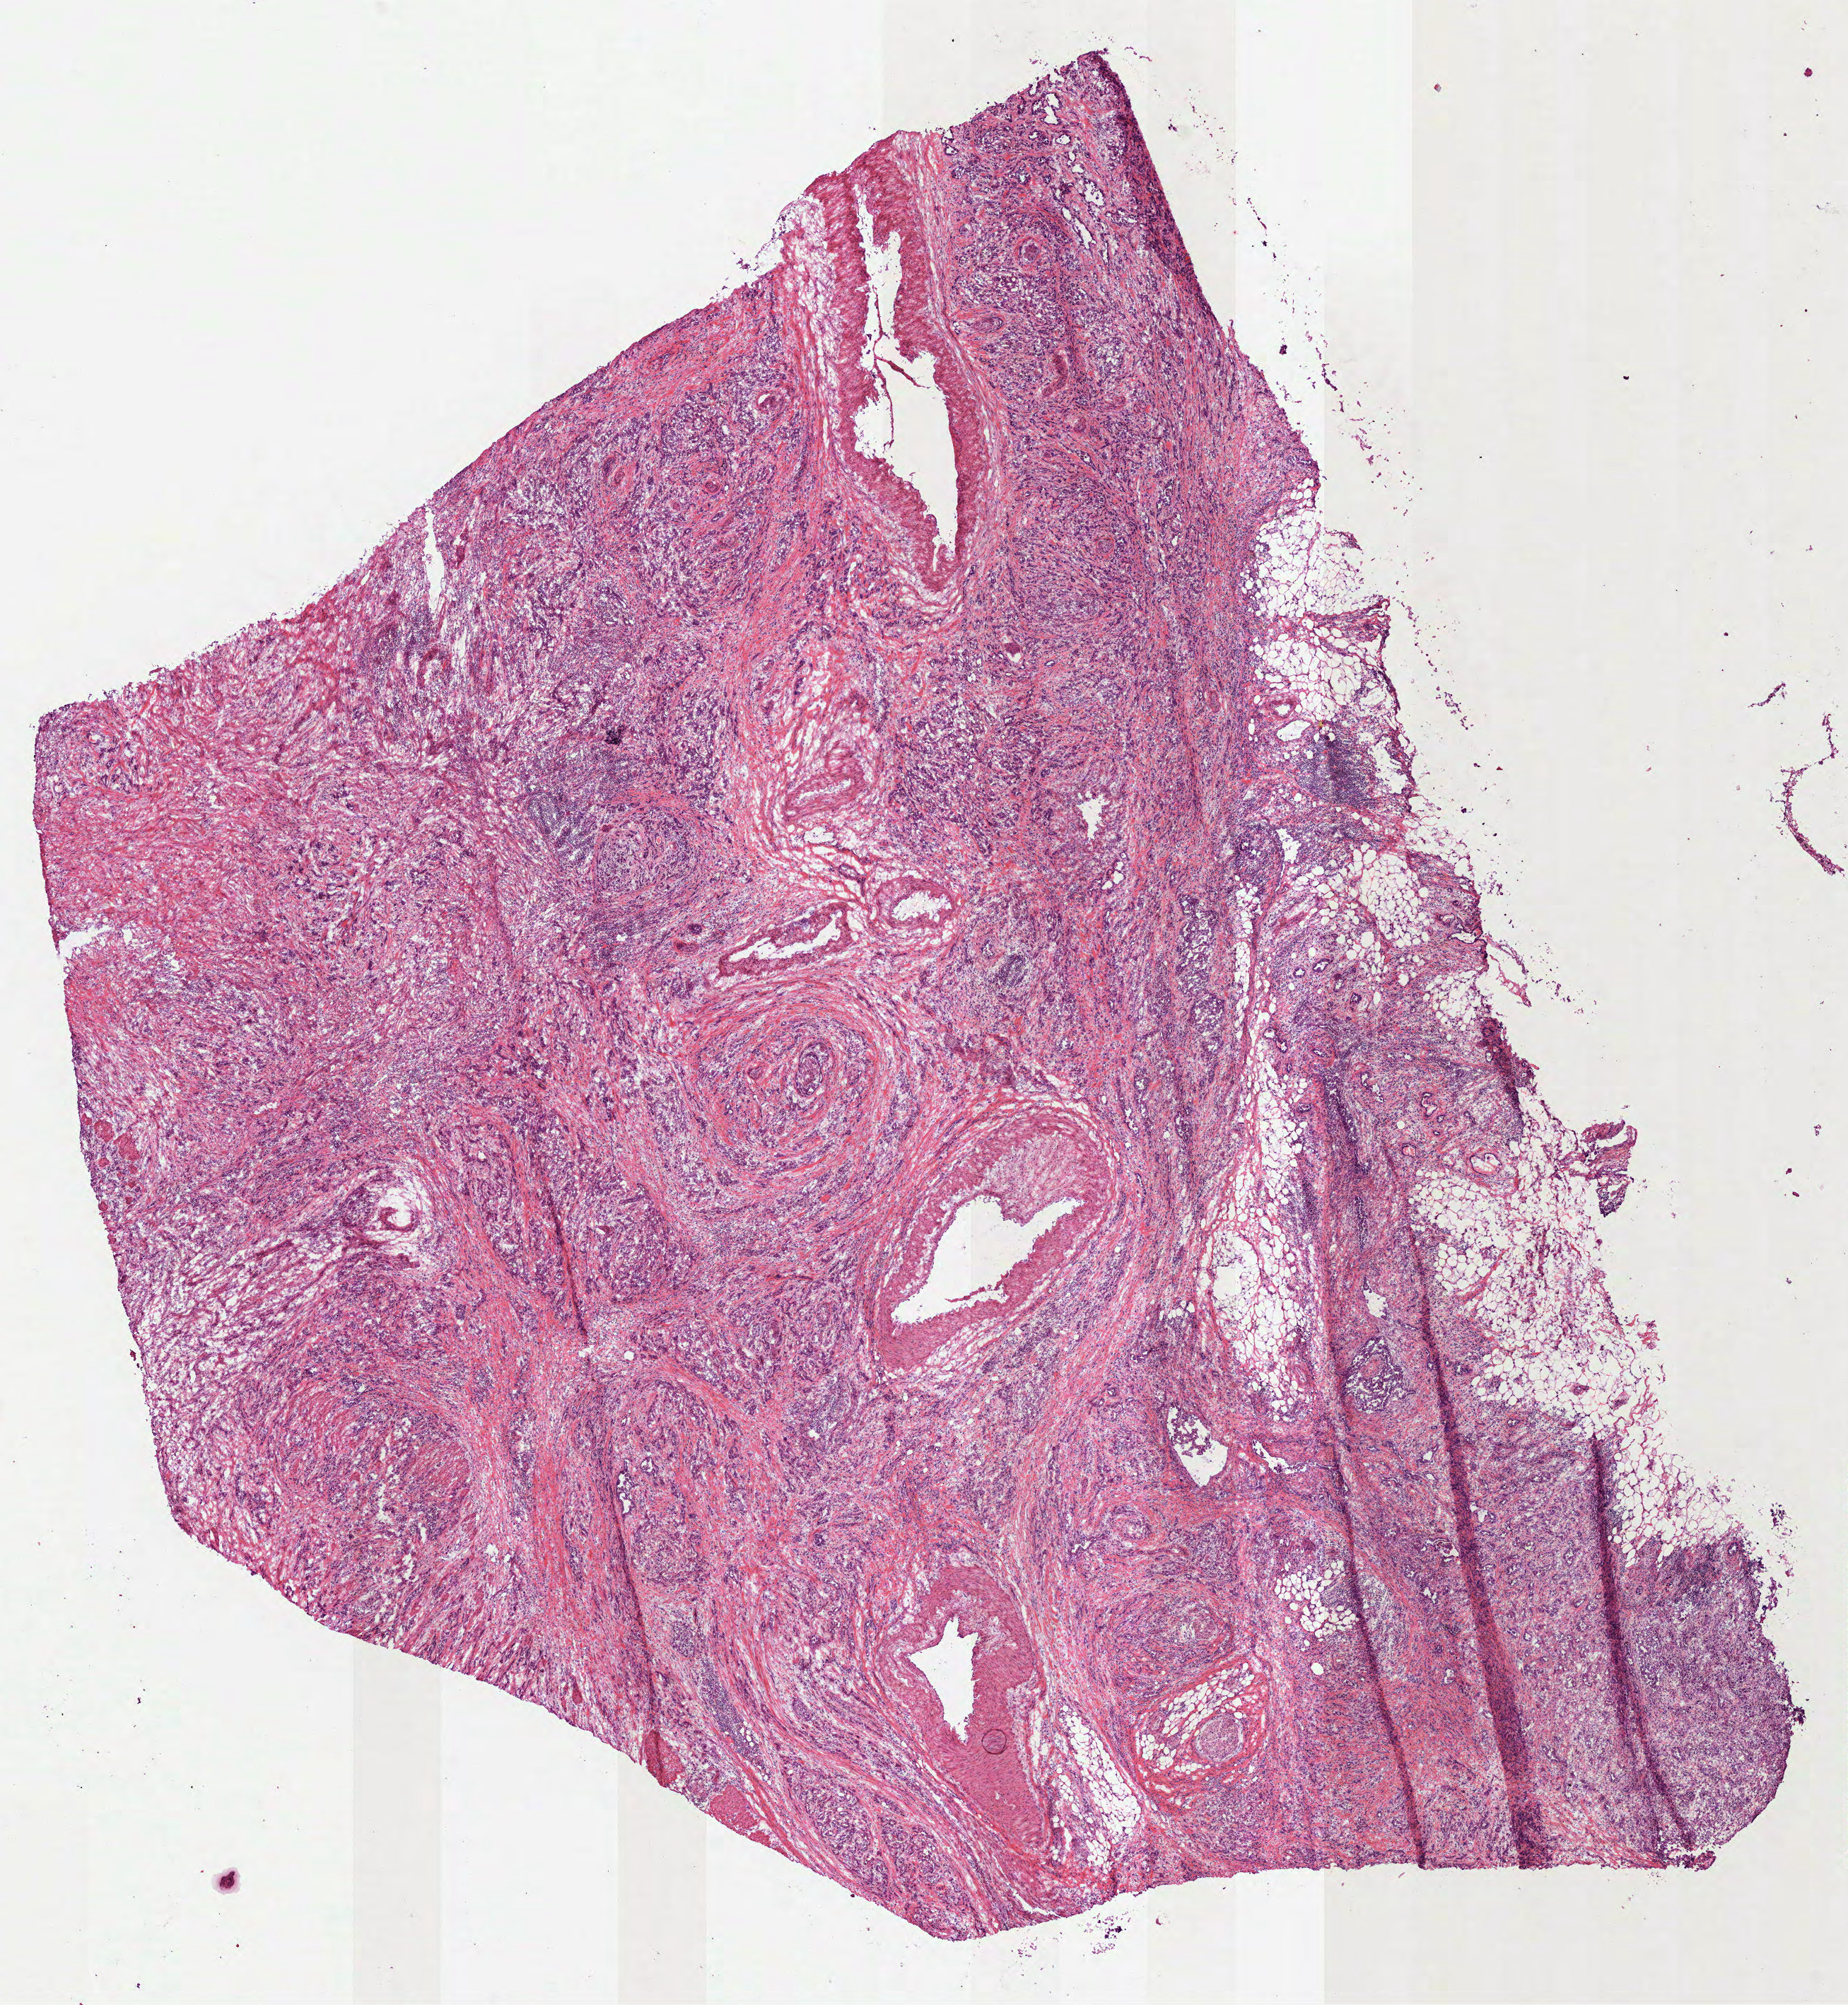
Whole-slide histology image, H&E, shown as a low-resolution overview of the whole scanned area (about 10.5 x 11.4 mm, slide scanned at 40x); frozen section from the bottom of the tissue portion; primary tumour sample from the stomach. Patient: female, age at initial diagnosis 61 years. Histologic grade: G3 (poorly differentiated). Slide review estimates, as recorded: tumour cells 85%, tumour nuclei 80%, normal cells 0%, stromal cells 15%, necrosis 0%.
AJCC pathologic stage: II (6th edition). Pathologic diagnosis: Adenocarcinoma, intestinal type (gastric antrum).